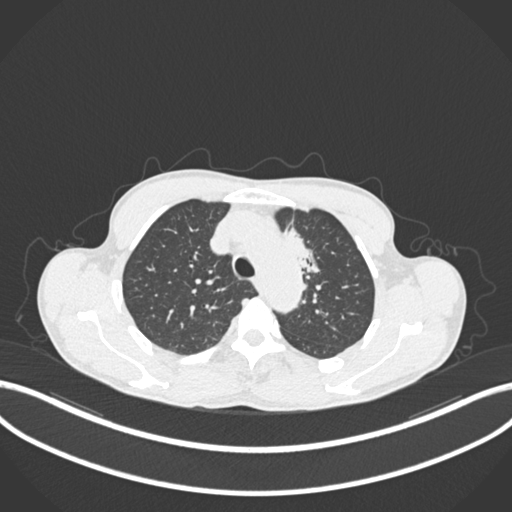
Chest CT, one axial slice; lung window (W 1500 / L -600 HU); 512 × 512 image matrix, field of view 400 × 400 mm. Male patient, age 58 years. From the clinical record (not read from this slice): clinical TNM (as recorded): T1c N1 M0.
Annotated regions visible in this slice (rectangle marked by the reading radiologist):
- lung tumour (recorded histology: adenocarcinoma): bounding box [x1, y1, x2, y2] px = [278, 223, 319, 279]